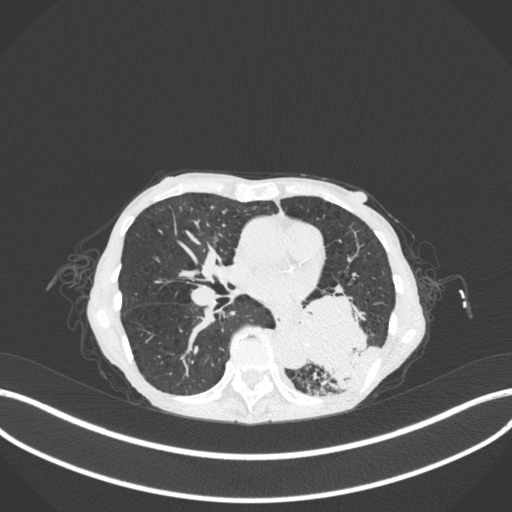
Chest CT, one axial slice; slice 133 of 347 in the series (ordered by position); reconstruction kernel B31f; 120 kVp; lung window (W 1500 / L -600 HU); 1 mm slice thickness; 512 × 512 image matrix. Patient: female, 70 years. Case-level facts recorded for this patient, not image findings: clinical TNM (as recorded): T3 N0 M0.
Structures marked on this image (rectangle marked by the reading radiologist):
- lung tumour (recorded histology: small cell carcinoma): bounding box (x1, y1, x2, y2) in pixels: (286, 276, 367, 387)